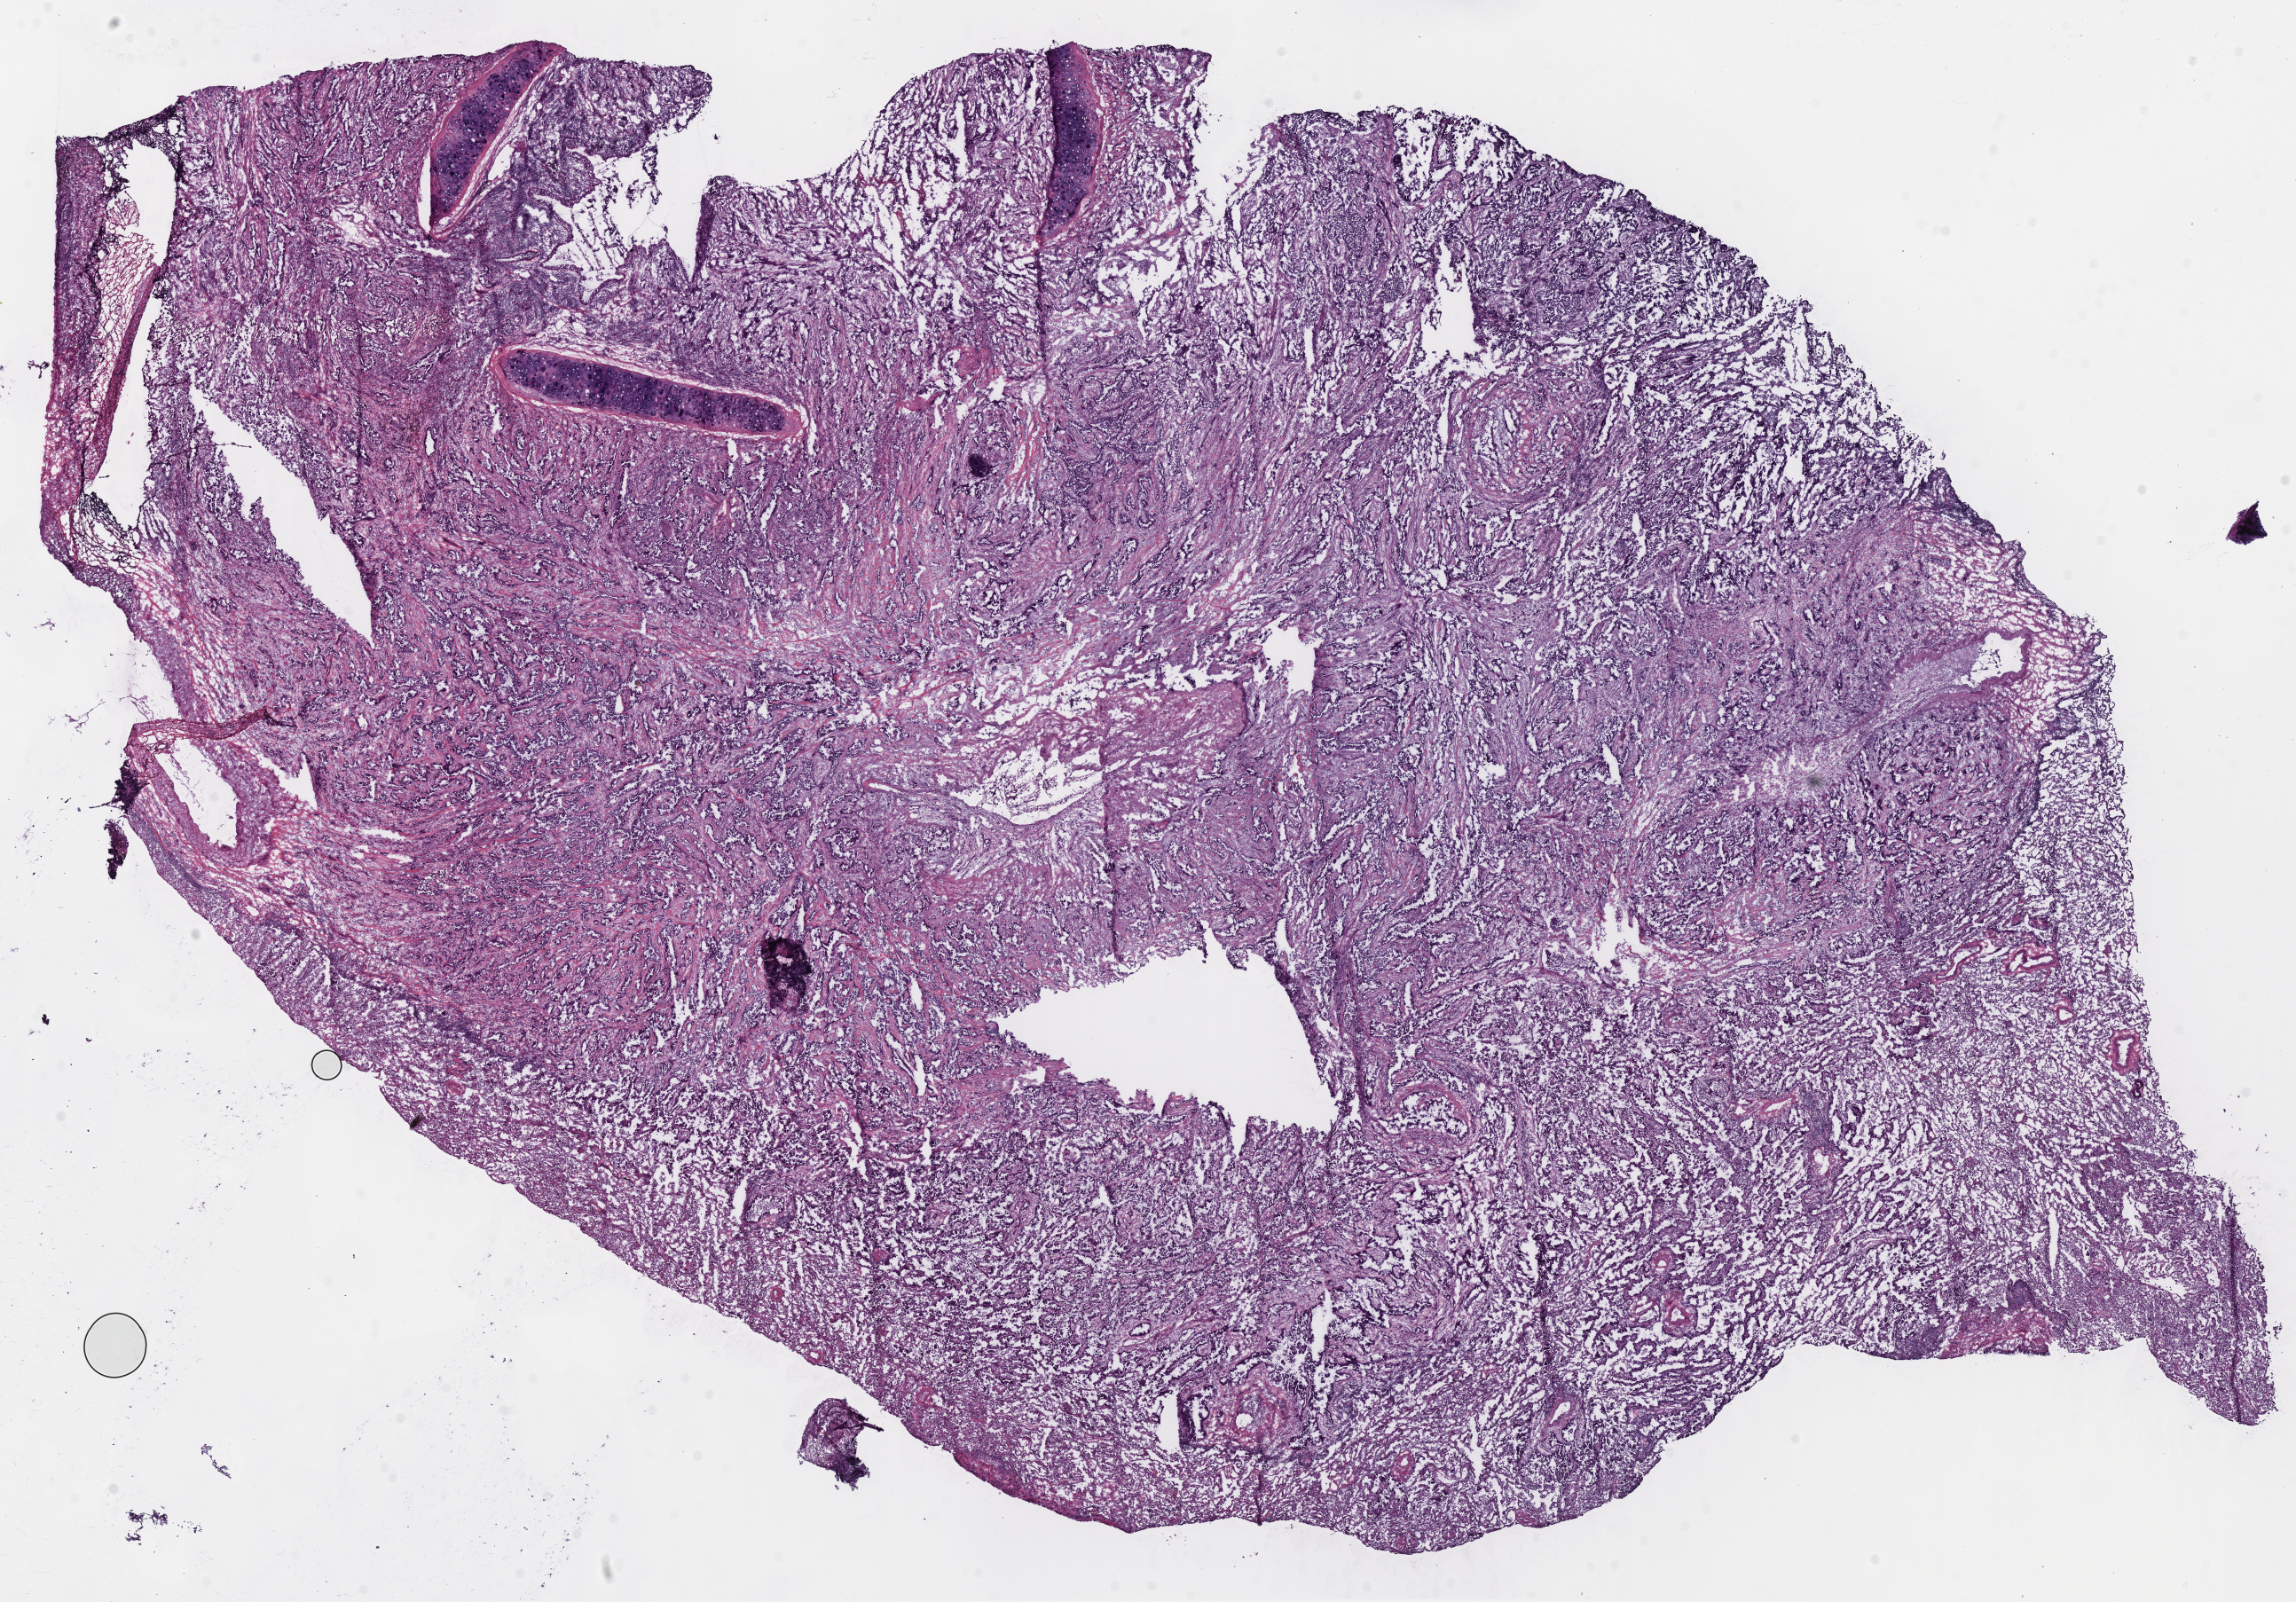
Whole-slide histology image, H&E — shown as a low-resolution overview of the whole scanned area (about 20.4 x 14.2 mm). Frozen section from the bottom of the tissue portion. Lung, primary tumour sample. Patient: female, age at initial diagnosis 62 years.
Histologic diagnosis: Papillary adenocarcinoma, NOS (lower lobe, lung).